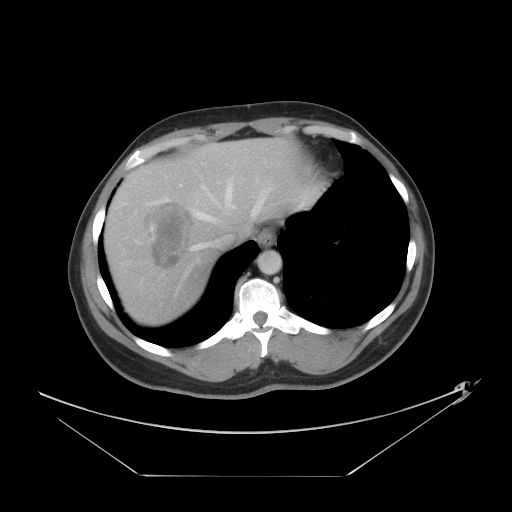
Contrast-enhanced abdominal CT, one axial slice. Slice 35 of 44 in the series (ordered by position). Reconstruction kernel STANDARD. Intravenous contrast given. Soft-tissue window (W 400 / L 40 HU). 512 × 512 image matrix. Male patient, age 49 years. From the clinical record (not read from this slice): diagnosis: colorectal cancer liver metastases, imaged before liver resection; multiple liver metastases: no; largest metastasis: 8.5 cm.
Structures marked on this image (expert manual segmentation):
- hepatic veins: box from (x=150, y=179) to (x=272, y=275) px
- liver: (x=104, y=137)–(x=324, y=328)
- planned liver remnant (the part of the liver to remain after resection): (x=196, y=138)–(x=325, y=242)
- portal vein (with intrahepatic branches): (x=150, y=226)–(x=154, y=230)
- liver metastasis: (x=147, y=202)–(x=194, y=271)